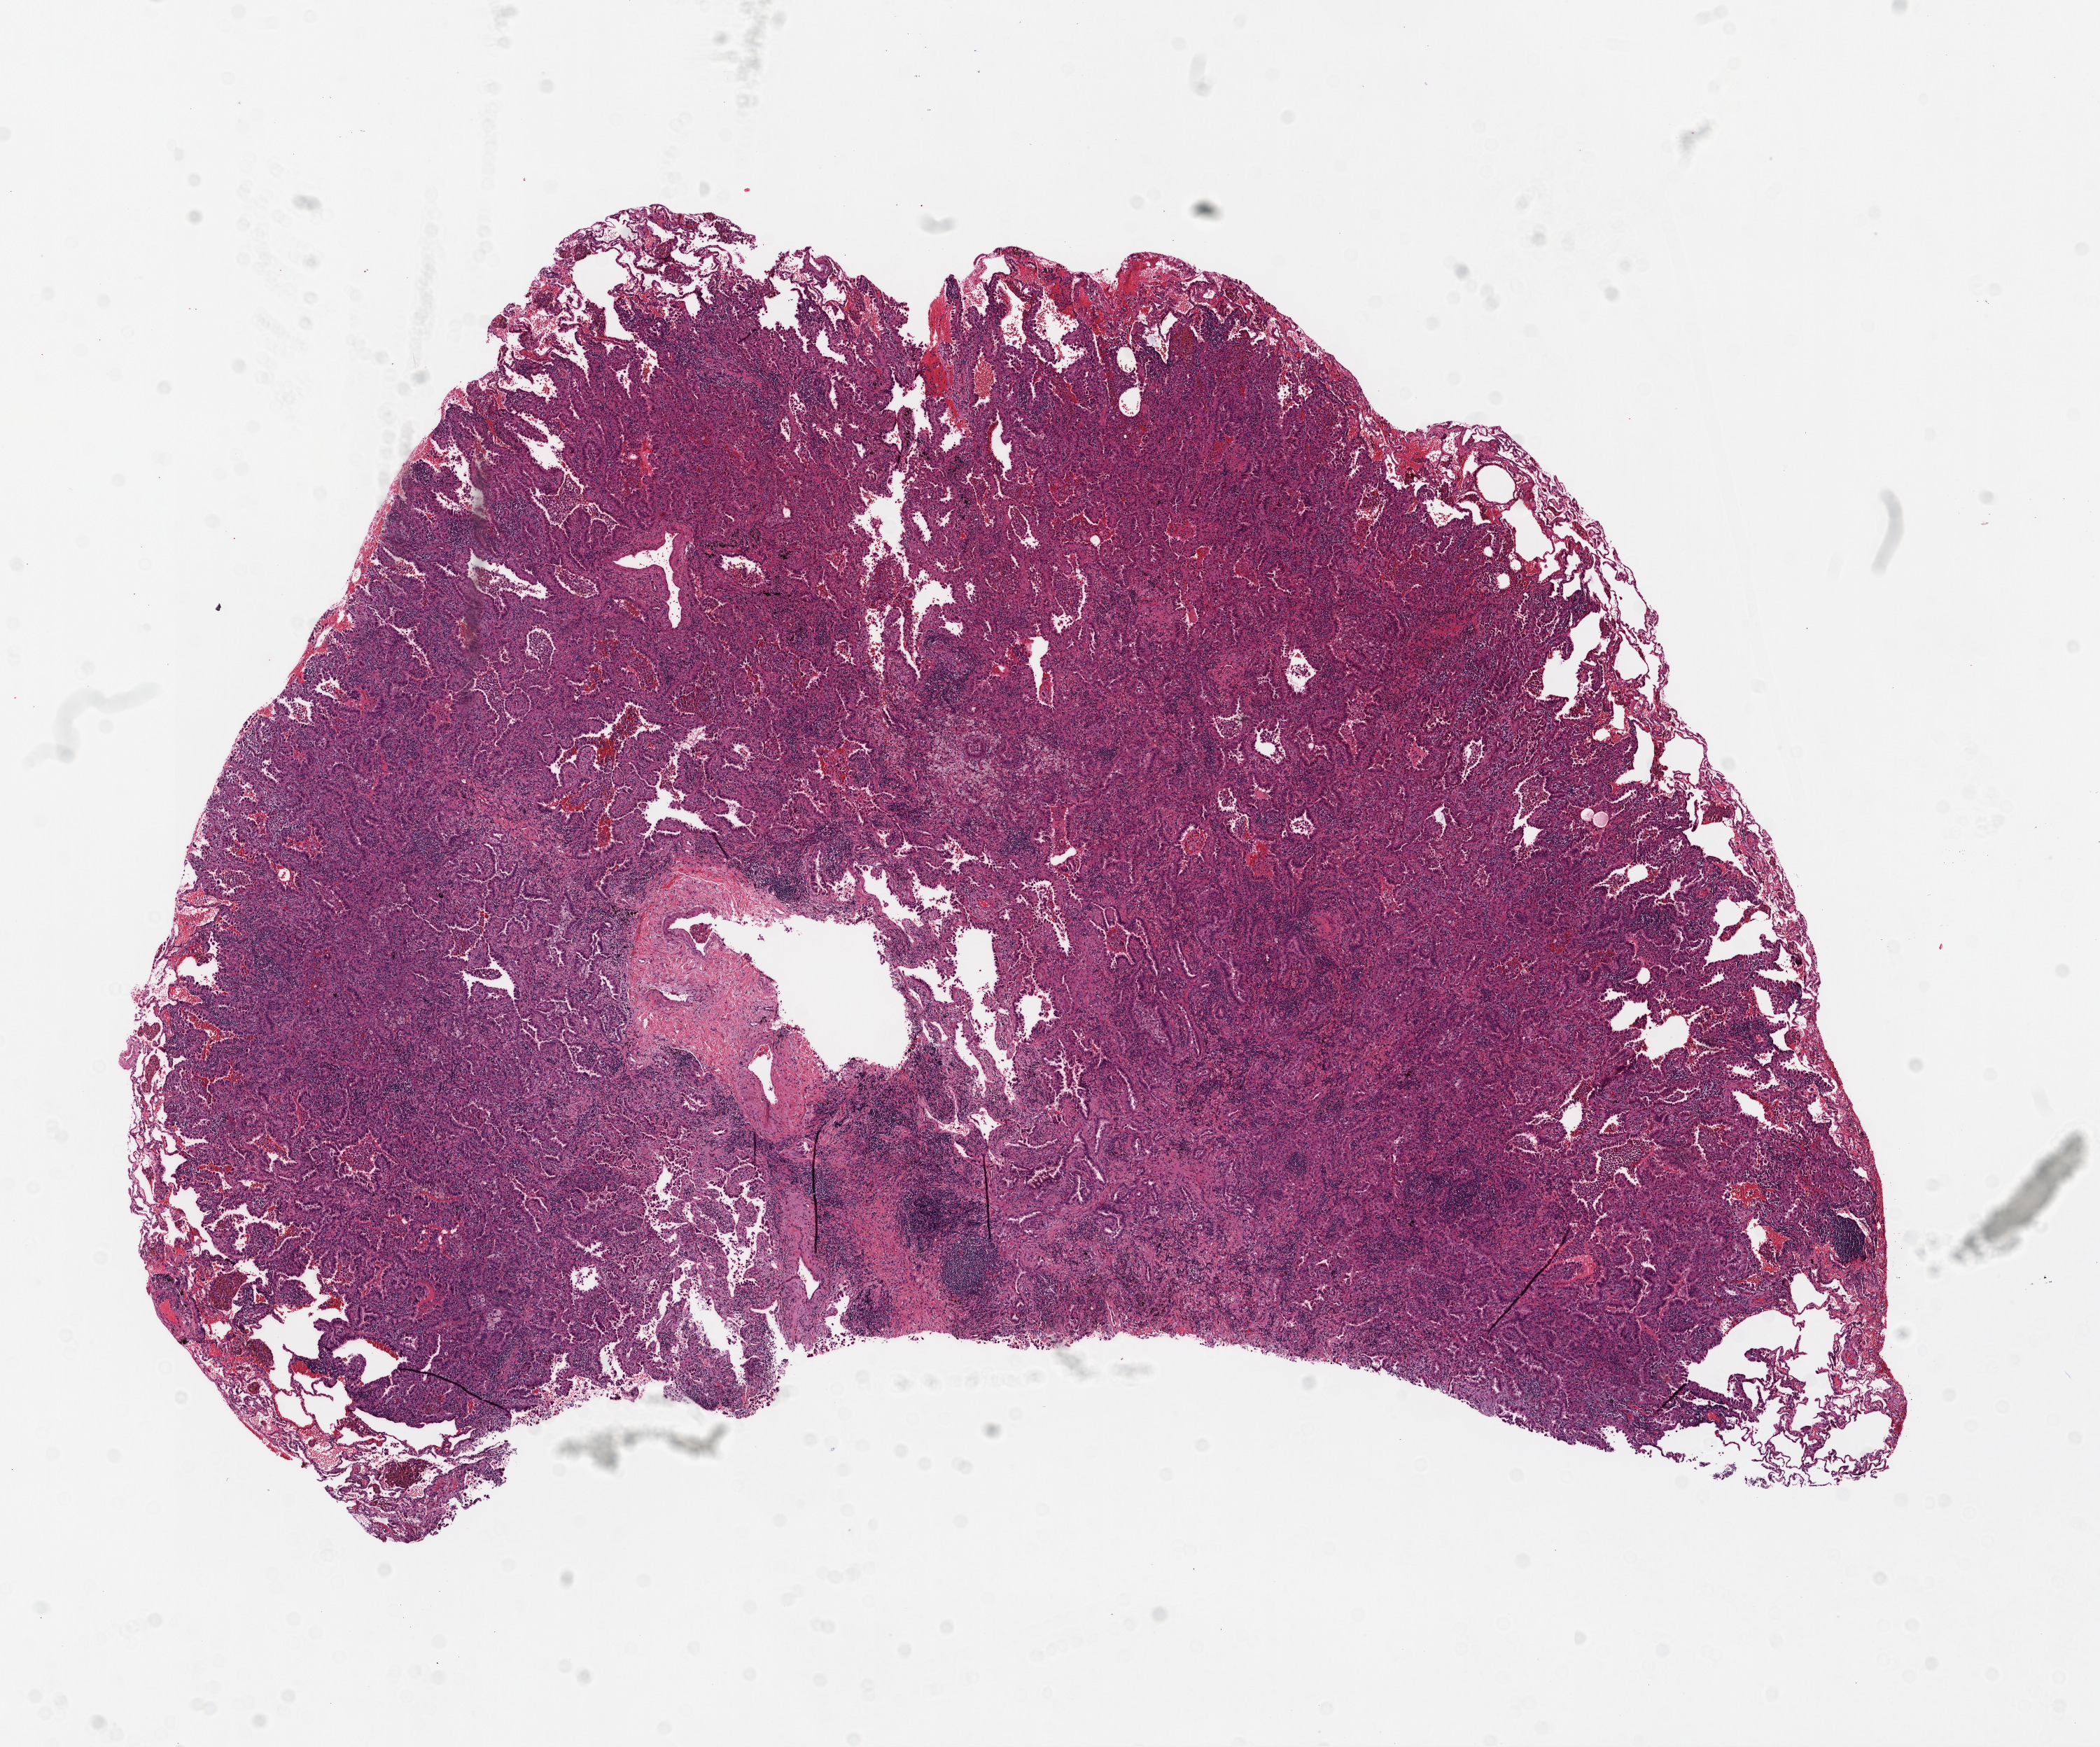
Whole-slide histology image, H&E-stained, shown as a low-resolution overview of the whole scanned area (about 12.0 x 10.0 mm); frozen section from the top of the tissue portion; sample: primary tumour, lung. Female patient; age at initial diagnosis 69 years. Slide review estimates, as recorded: tumour cells 93%, tumour nuclei 80%, normal cells 5%, stromal cells 2%, necrosis 0%. Infiltration values recorded for this section: lymphocyte infiltration 15%, monocyte infiltration 2%.
AJCC pathologic stage: IA. Diagnosis: Adenocarcinoma, NOS (upper lobe, lung). TNM: T1 N0 M0.